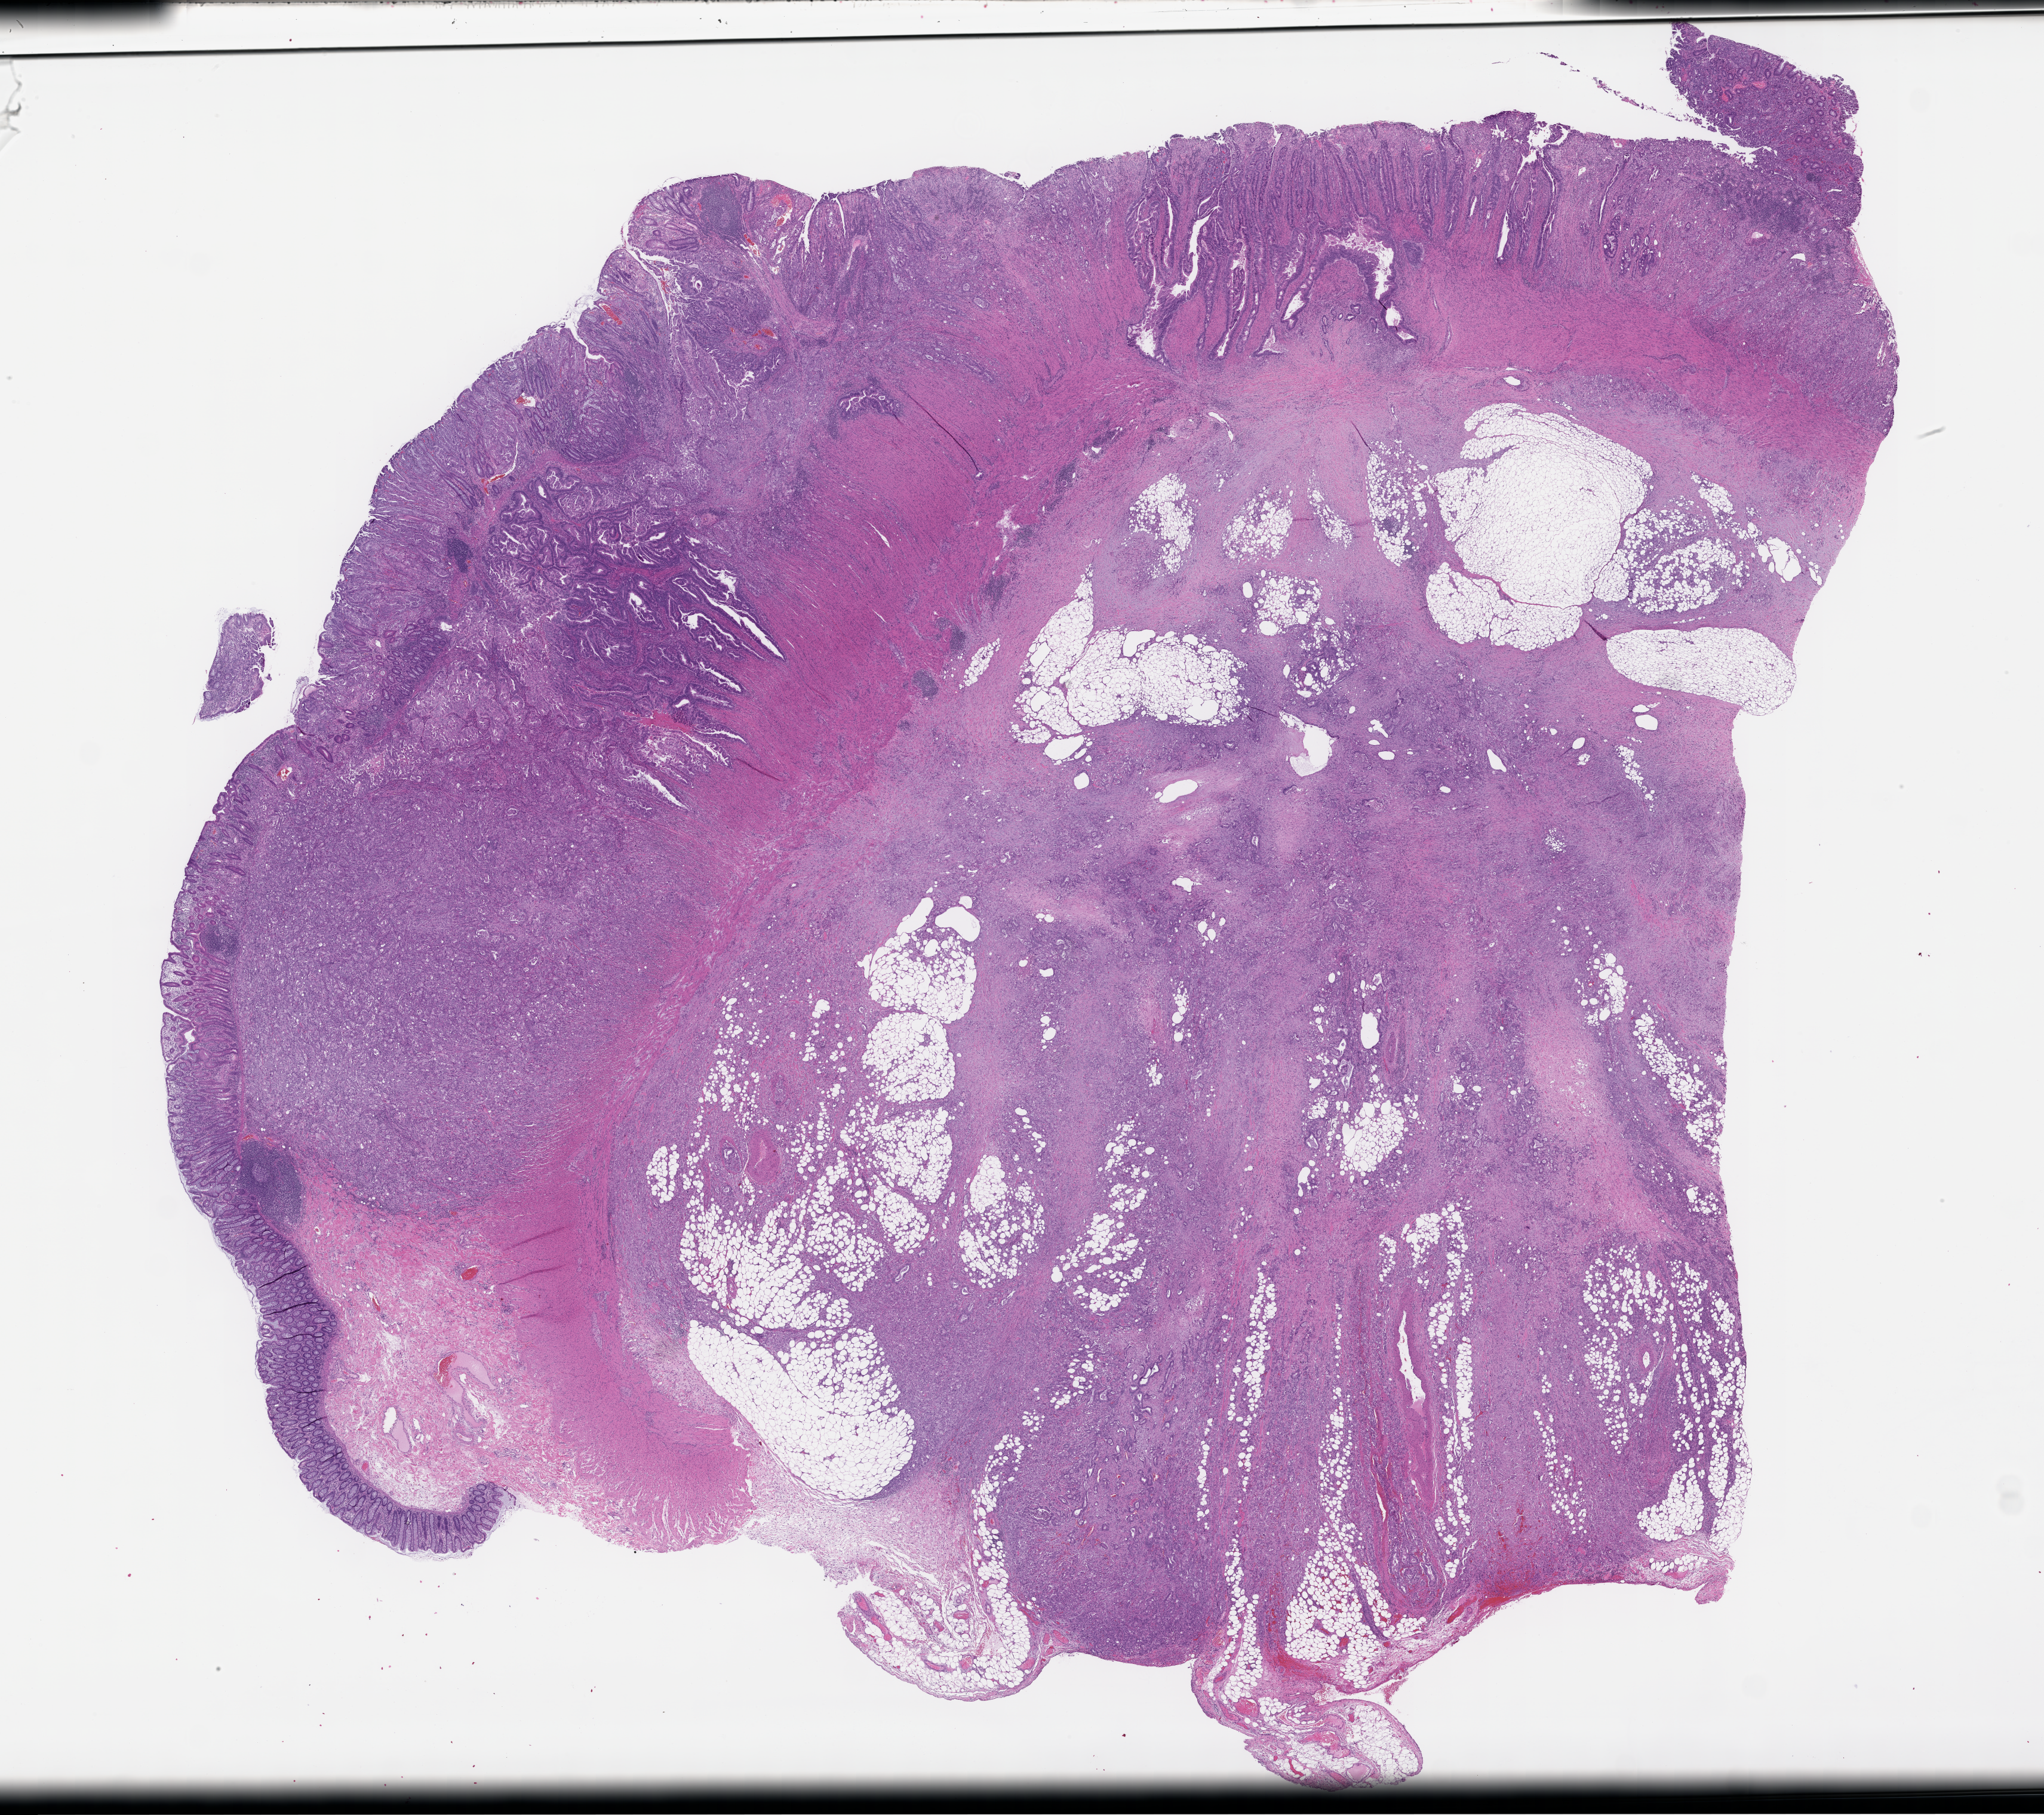
Digitized haematoxylin and eosin-stained section, a low-resolution overview of the entire scanned area, about 27.6 x 24.5 mm, FFPE section, site: colon. Male patient.
This section: primary tumor. Diagnosis: Colorectal Carcinoma.